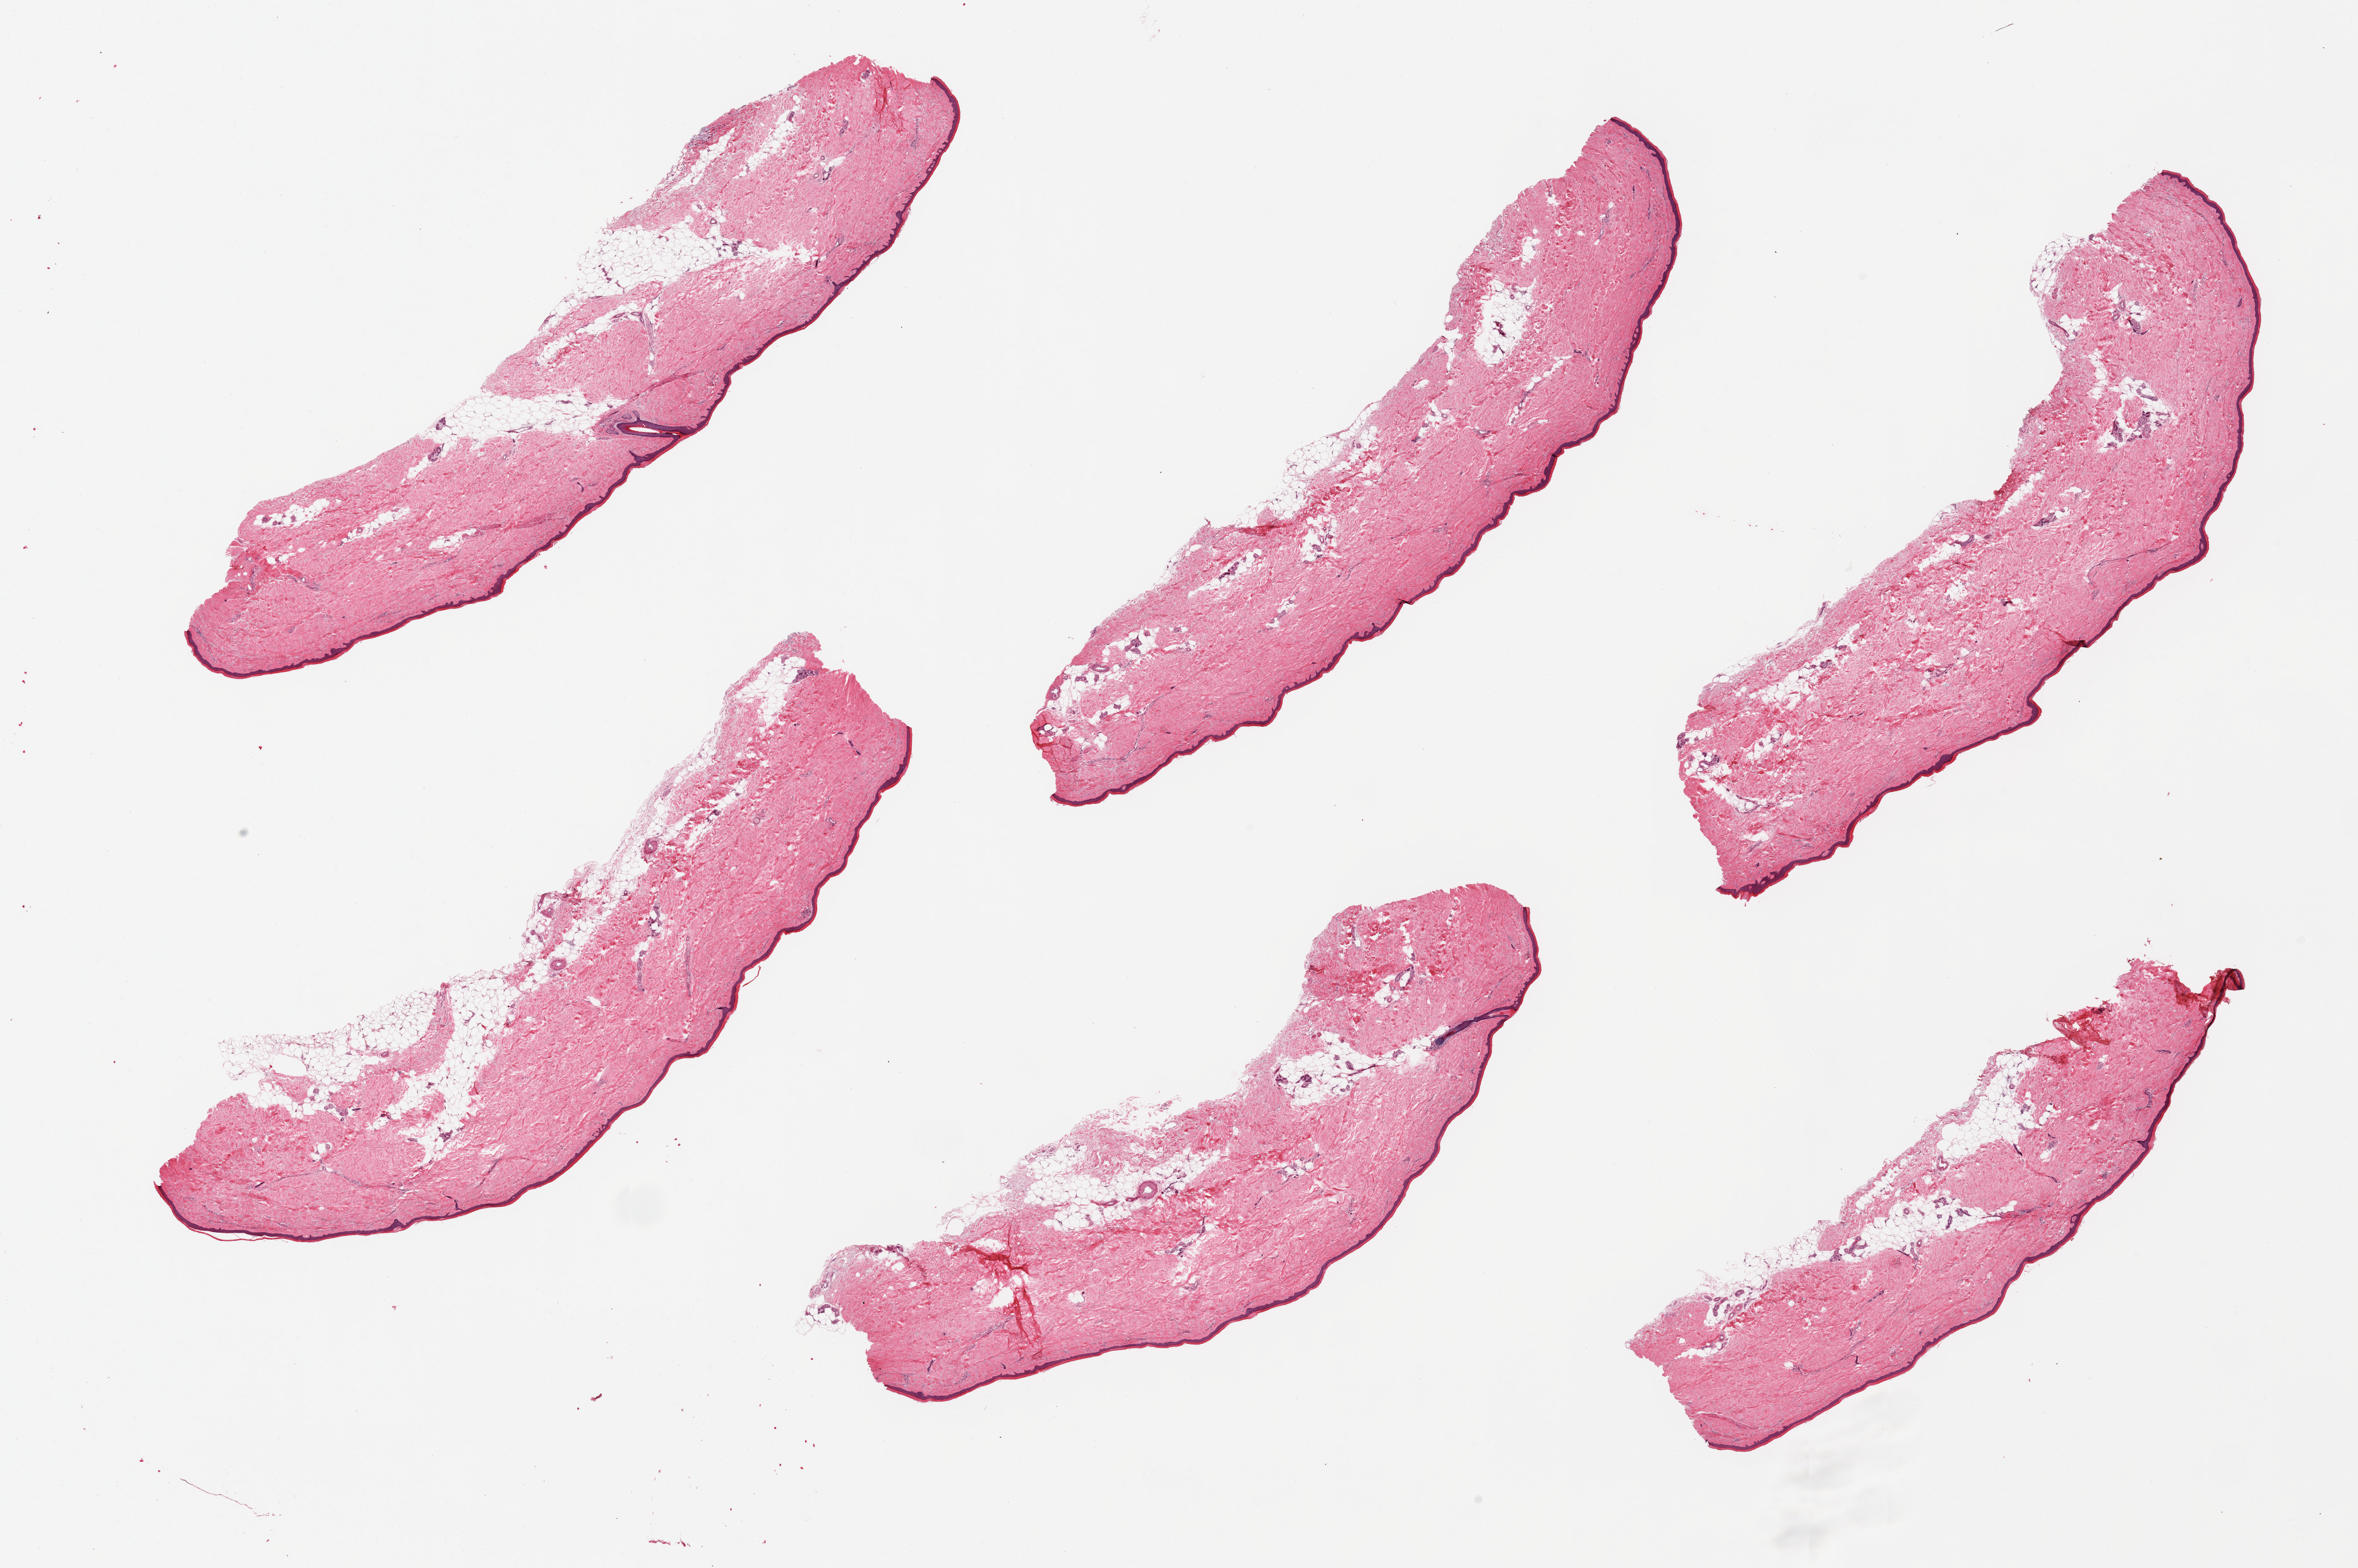
H&E whole-slide image, low-resolution overview of the scanned area, about 29.5 x 19.6 mm (slide scanned at 20x). PAXgene-fixed paraffin-embedded (PFPE) section. Sampled site (target tissue): skin of lower leg. Tissue donor sample. Donor: female.
- pathologist's review note for this sample: 6 pieces, trace adherent dermal fat, squamous epithelium is ~40 microns